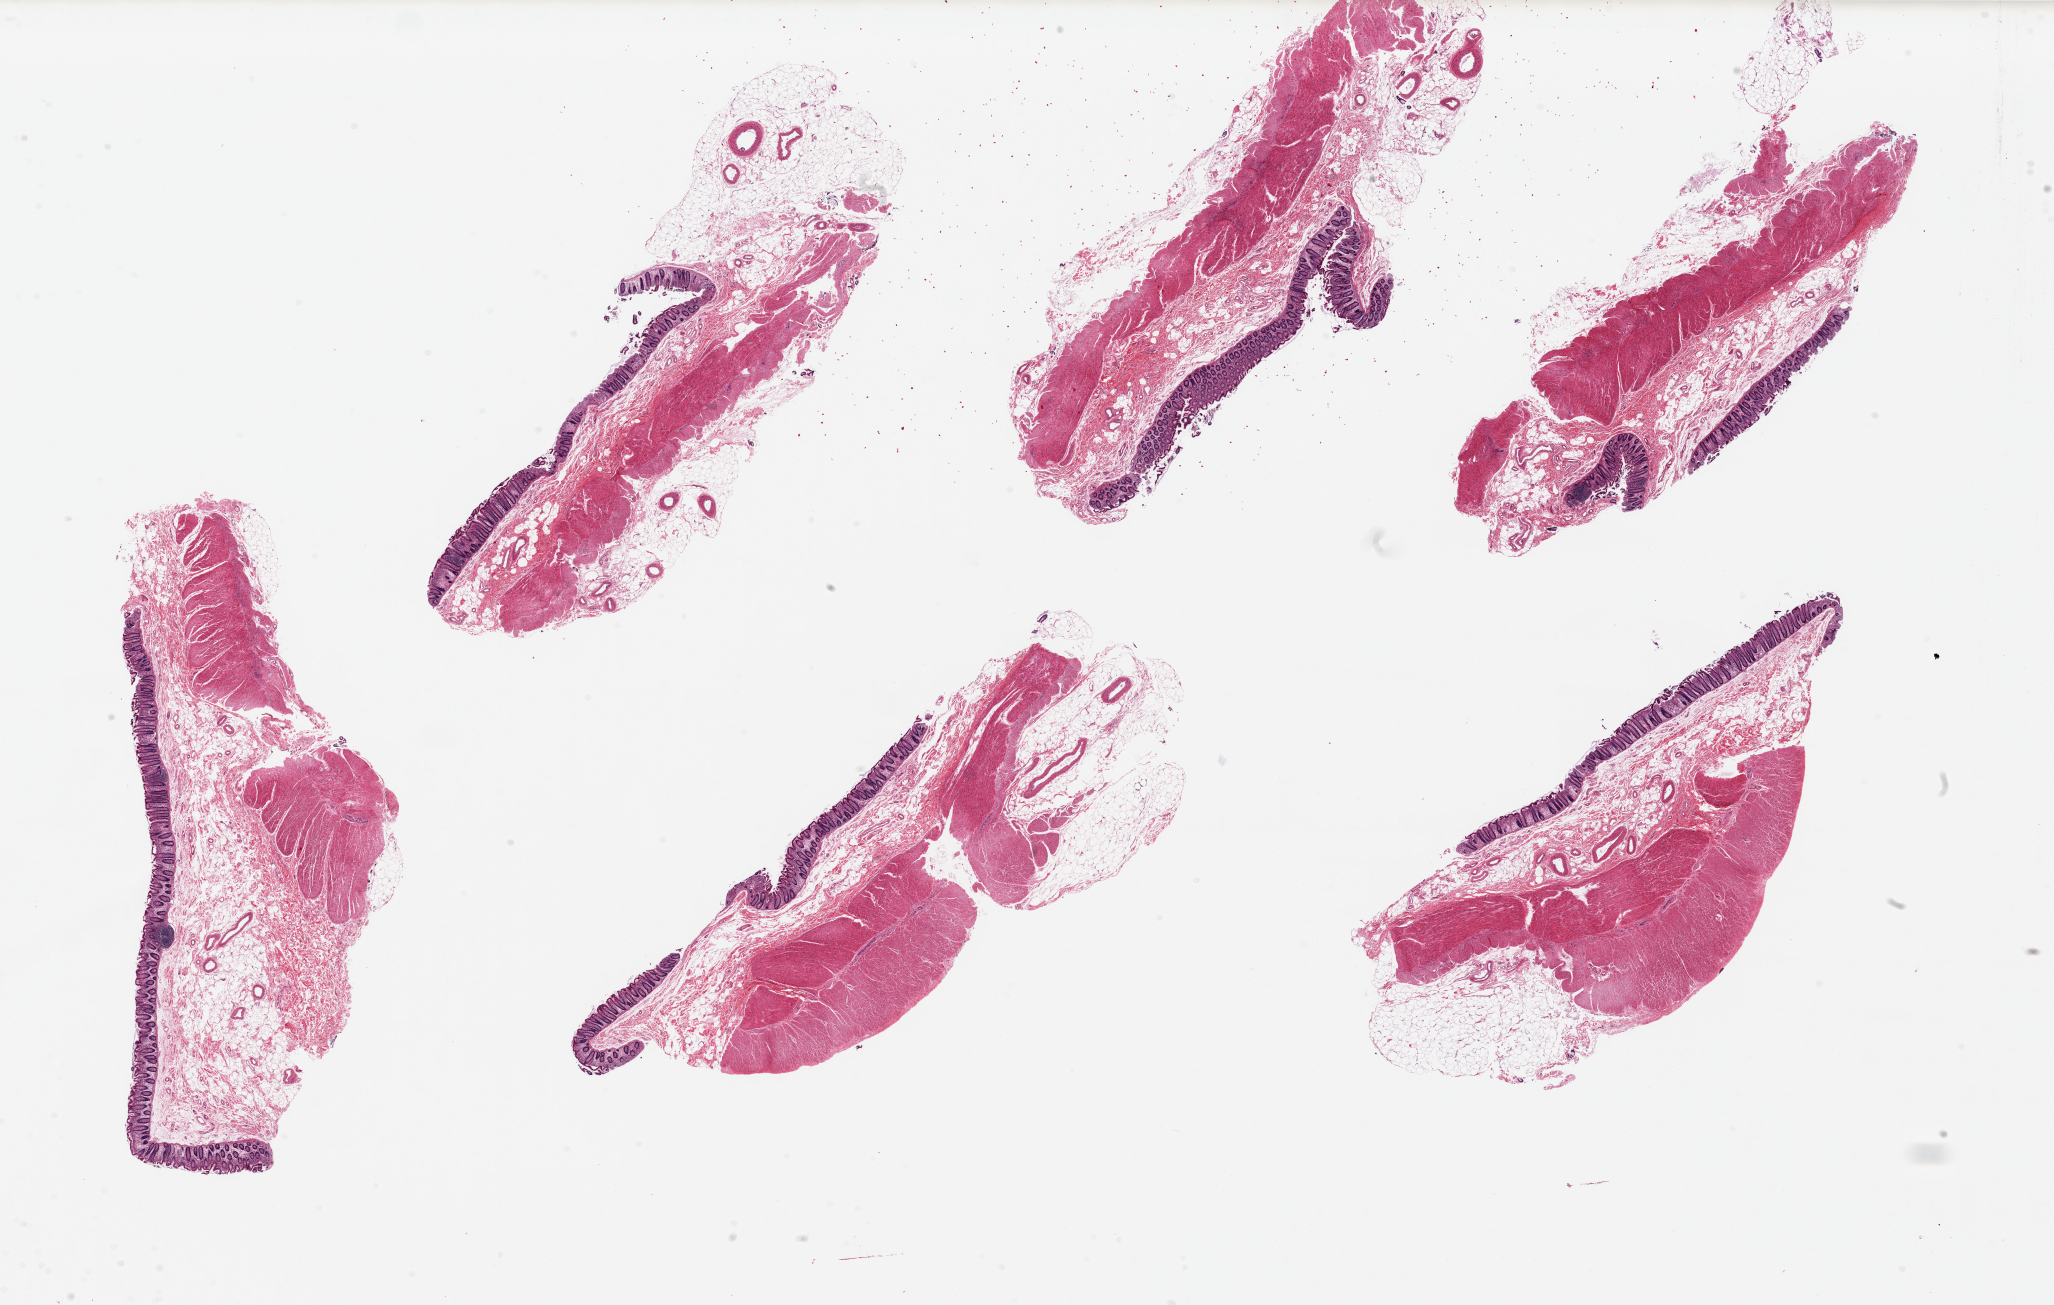
H&E whole-slide image, brightfield, low-resolution overview of the scanned area, about 32.5 x 20.6 mm (acquisition: 20x scan). PAXgene-fixed, paraffin-embedded tissue. Target tissue: transverse colon. Tissue donor sample.
Review note (as recorded): 6 pieces ~10x3mm. Mucosa variably but moderately preserved, ~10-15% of thickness.